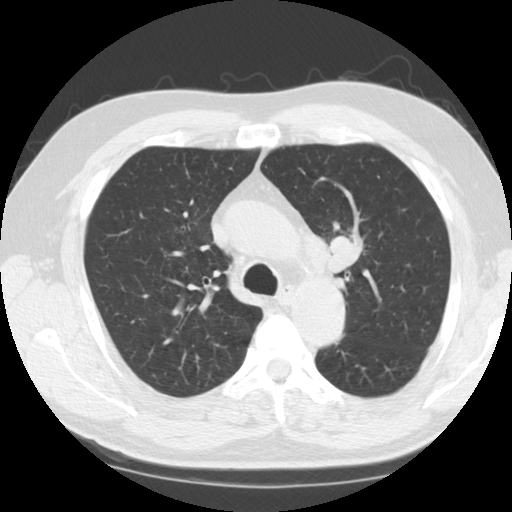
Axial slice from a low-dose chest CT screening exam. Third annual screen. Lung window (W 1500 / L -600 HU). 512 × 512 image matrix. Male participant, aged 60 years at enrolment.
Expert reader's lesion annotation, bounding box (x1, y1, x2, y2) in pixels: (316, 223, 369, 278). Reader record for this screening exam (exam-level; its link to the box is not recorded): non-calcified nodule or mass ≥4 mm, left upper lobe, 24 × 21 mm, smooth margins, soft tissue attenuation, pre-existing on the prior screen: no. Official screen result: positive, other.